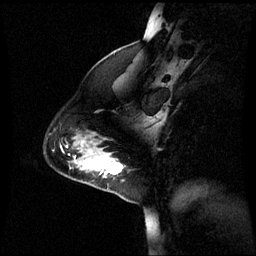
Breast MRI (dynamic contrast-enhanced), one sagittal slice. Slice 17 of 60 in the series (ordered by position). Dynamic contrast-enhanced series, image 2 of 3 at this slice position (ordered by acquisition). 1.5 T. TE 4.2 ms, TR 8.9 ms. 2.2 mm slice thickness. 256 × 256 image matrix, field of view 240 × 240 mm. Female patient, age 44 years. From the clinical record (not read from this slice): setting: breast cancer imaged before/during neoadjuvant chemotherapy; receptor status: triple-negative.
Annotated regions visible in this slice (semi-automatic segmentation, software-assisted and operator-edited):
- analysis volume of interest (the breast-tissue region the enhancement analysis was run in; not a lesion): box from (x=76, y=150) to (x=125, y=185) px
- tumour enhancement mask (voxels above the 70 % enhancement threshold inside the analysis volume of interest): (x=86, y=158)–(x=123, y=175)